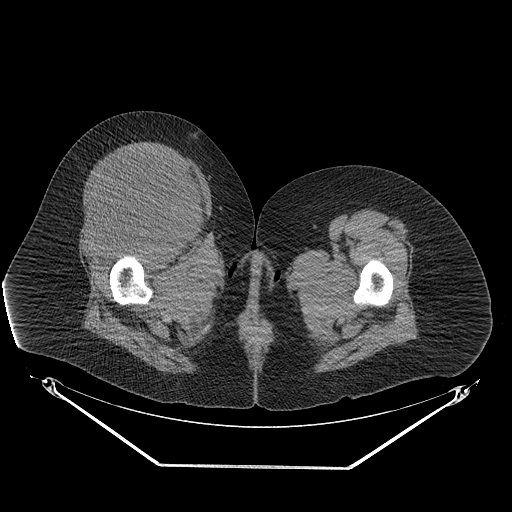
CT of an extremity soft-tissue mass (from a PET/CT study), one axial slice. Slice 49 of 267 in the series (ordered by position). Soft-tissue window (W 400 / L 40 HU). 3.75 mm slice thickness. 512 × 512 image matrix, field of view 500 × 500 mm. Female patient. Case-level facts recorded for this patient, not image findings: histological type: malignant solitary fibrous tumor; grade: intermediate; site of the primary tumour: right thigh.
Outlined on this slice (expert contour drawn on MRI and transferred to this co-registered scan by the dataset authors):
- gross tumour volume including surrounding oedema: bounding box [x1, y1, x2, y2] px = [75, 149, 204, 245]
- gross tumour volume (mass): [80, 149, 202, 243]